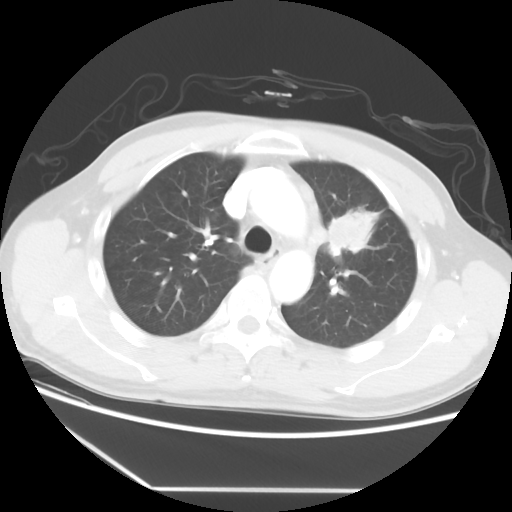
Chest CT, one axial slice. Slice 39 of 56 in the series (ordered by position). Reconstruction kernel STANDARD. 120 kVp. Lung window (W 1500 / L -600 HU). 5 mm slice thickness. 512 × 512 image matrix, field of view 373 × 373 mm. Male patient, age 53 years. From the clinical record (not read from this slice): clinical TNM (as recorded): T2a N1 M1b.
Outlined on this slice (bounding box drawn by a radiologist):
- lung tumour (recorded histology: adenocarcinoma): bounding box [x1, y1, x2, y2] px = [324, 208, 381, 254]